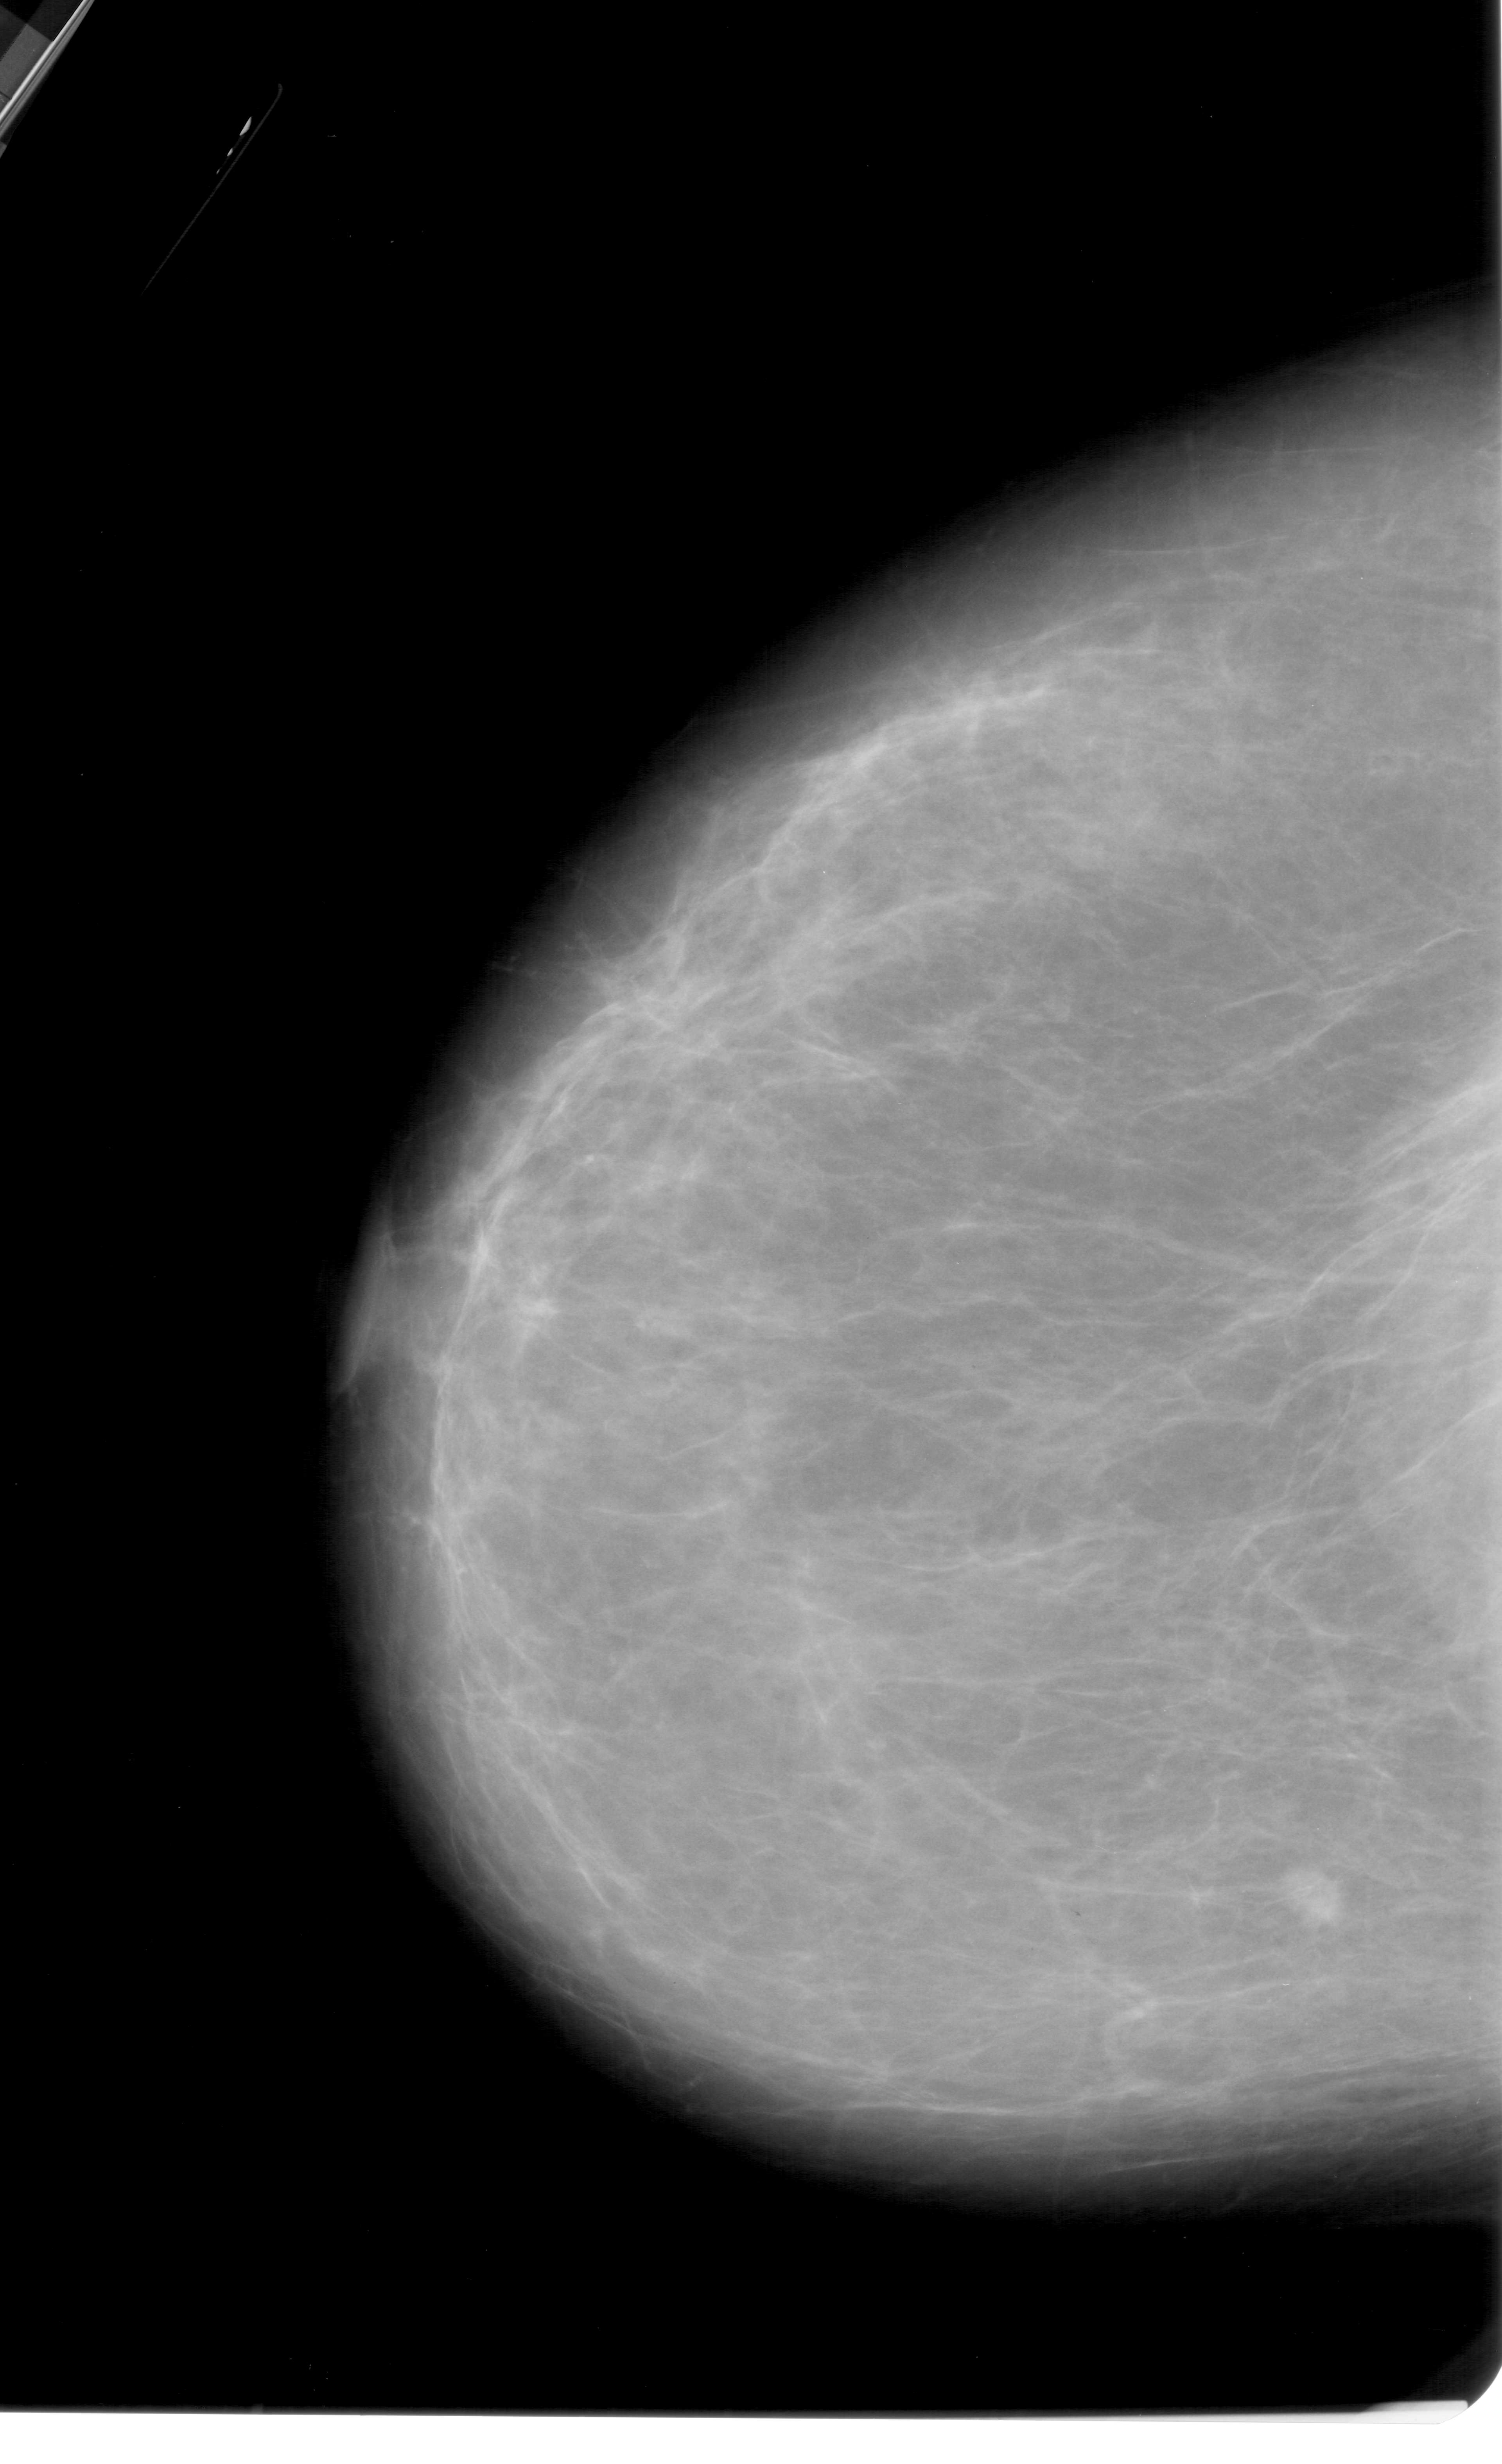
Scanned film-screen mammogram; left breast; craniocaudal (CC) view; breast composition: scattered fibroglandular densities (BI-RADS density category 2 of 4); 1502 × 2464 image matrix.
Expert-marked regions of interest on this film, with their recorded descriptors:
- mass, shape oval, margins ill defined; BI-RADS assessment category 5; pathology (as recorded): malignant: bounding box (x1, y1, x2, y2) in pixels: (1262, 1862, 1352, 1939)